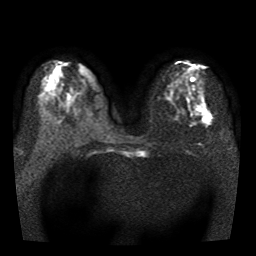
Breast MRI, one axial slice; slice 17 of 41 in the series (ordered by position); diffusion-weighted series; image 2 of 3 stored at this slice position (different b-values; order by instance number); 1.5 T; 5 mm slice thickness; 256 × 256 image matrix, field of view 330 × 330 mm. Female patient.
Structures marked on this image (expert manual segmentation):
- tumour on diffusion-weighted imaging: bounding box <203,104,211,125> (left, top, right, bottom; pixels)